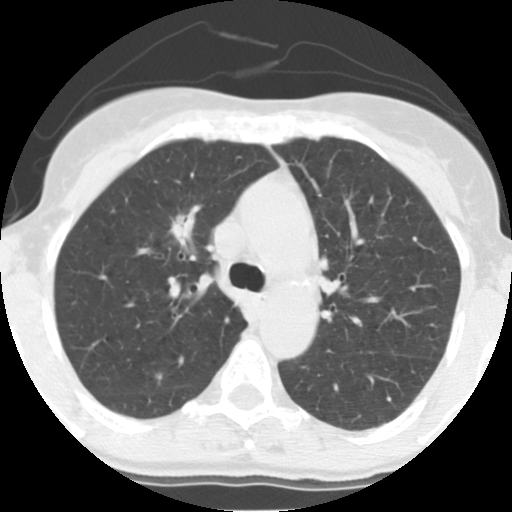
Low-dose screening chest CT, one axial slice. Slice 96 of 140 in the series (ordered by position). Reconstruction kernel STANDARD. Lung window (W 1500 / L -600 HU). 512 × 512 image matrix, field of view 280 × 280 mm.
Outlined on this slice (outlined manually by an expert reader):
- lesion 1 (tumor, upper lobe of right lung): box from (x=169, y=215) to (x=188, y=245) px